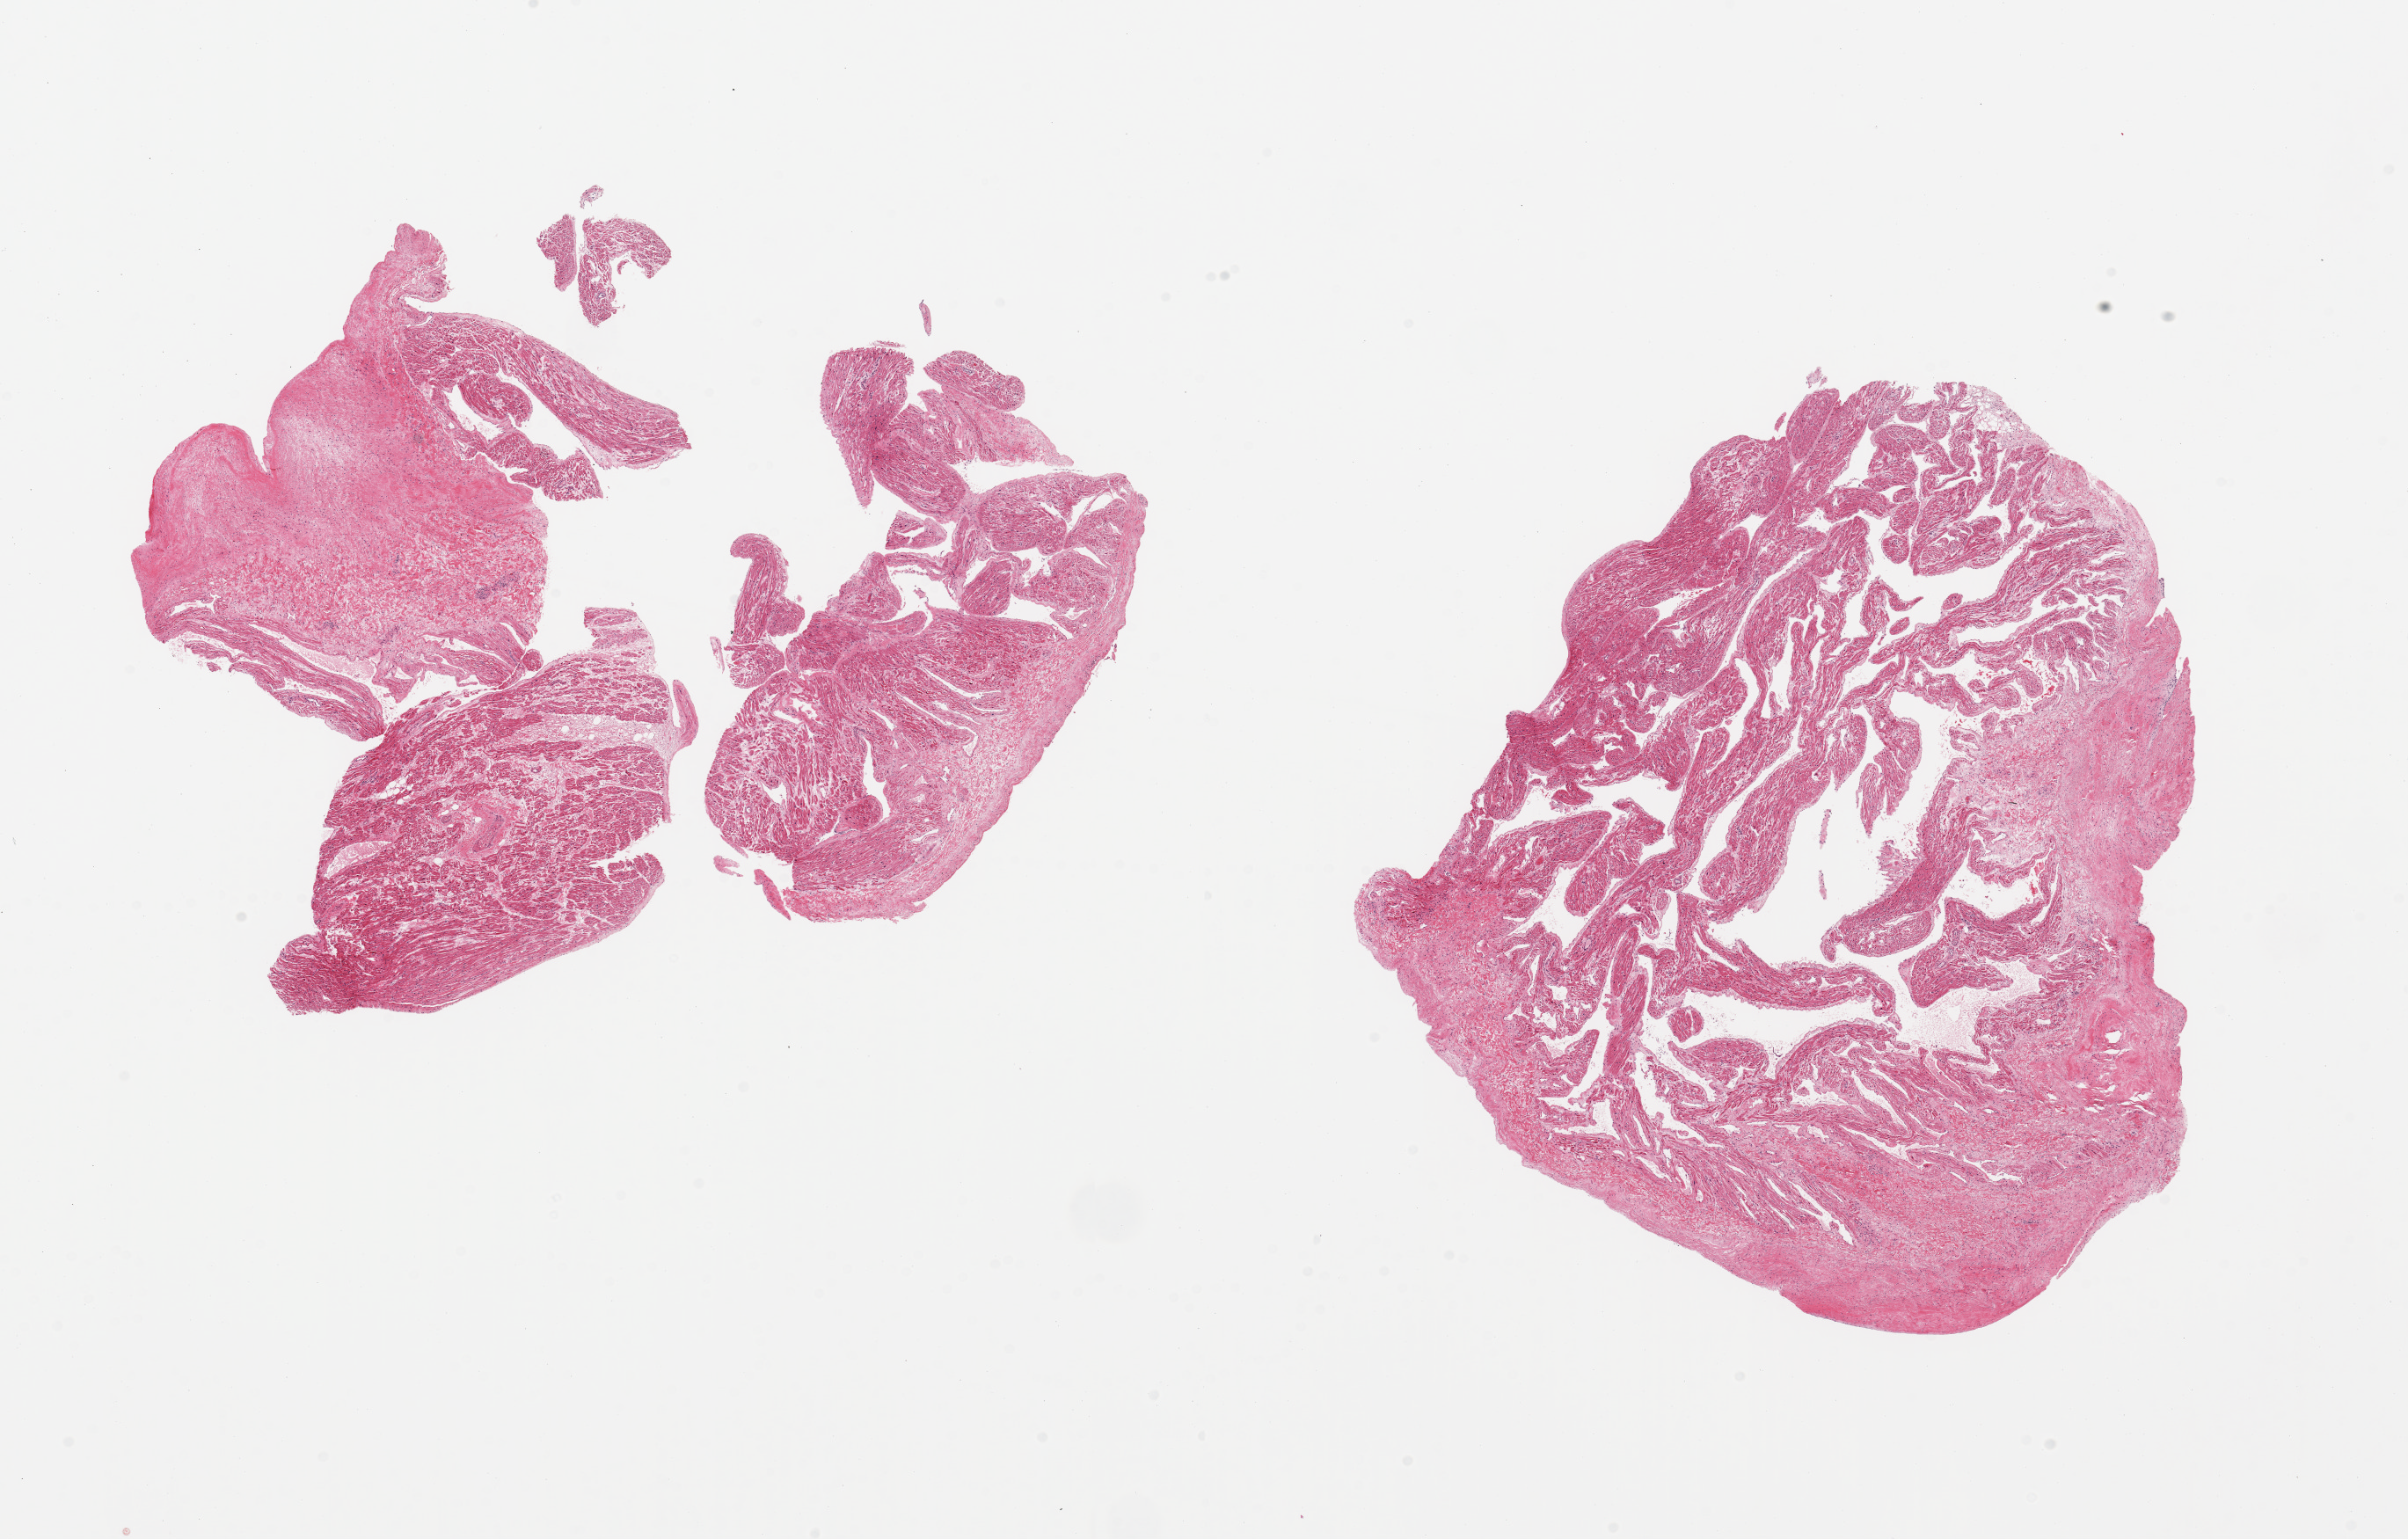
H&E whole-slide image — whole scanned area (about 21.7 x 13.8 mm) shown as a low-resolution overview, PAXgene-fixed, paraffin-embedded tissue, section of auricular appendage (target tissue), tissue donor sample. Male donor.
Review note (as recorded): 2 pieces, no abnormalities.